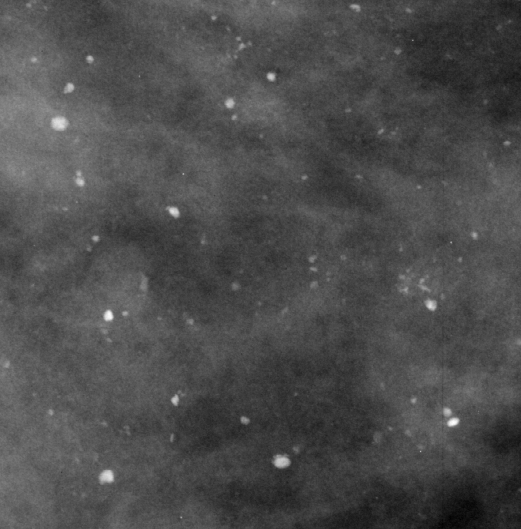
Region of interest cut from a scanned film mammogram (one marked finding), right breast, CC view, BI-RADS breast density category 4 (scale 1–4).
Marked abnormality: calcifications, morphology vascular / coarse / lucent center / round and regular / punctate, distribution regional; BI-RADS assessment category 2; subtlety rating 5 on a 1 (subtle) to 5 (obvious) scale; benign; no additional work-up was recommended (benign without callback).